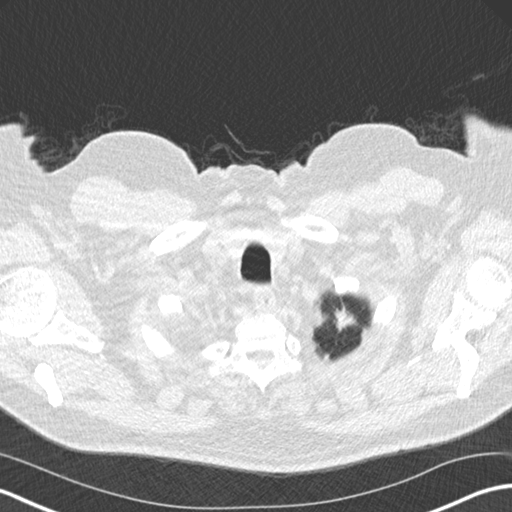
Low-dose screening chest CT, one axial slice. Slice 158 of 175 in the series (ordered by position). 120 kVp. Lung window (W 1500 / L -600 HU). 512 × 512 image matrix.
Annotated regions visible in this slice (manually delineated by an expert):
- lesion 1 (tumor, upper lobe of left lung): bounding box (x1, y1, x2, y2) in pixels: (334, 309, 356, 331)